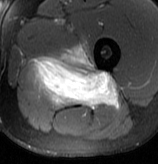
MRI of an extremity soft-tissue mass, one axial slice; slice 51 of 70 in the series (ordered by position); T2-weighted fat-saturated; MR volume resampled by the dataset authors to the PET/CT grid (not the native acquisition matrix); 158 × 164 image matrix, field of view 154 × 160 mm. Male patient. From the clinical record (not read from this slice): histological type: extraskeletal osteosarcoma; grade: high; site of the primary tumour: left adductur.
Annotated regions visible in this slice (expert contour drawn on MRI and transferred to this co-registered scan by the dataset authors):
- gross tumour volume (mass): box from (x=31, y=44) to (x=119, y=108) px